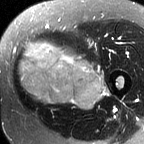
MRI of an extremity soft-tissue mass, one axial slice; slice 25 of 60 in the series (ordered by position); T2-weighted fat-saturated; MR volume resampled by the dataset authors to the PET/CT grid (not the native acquisition matrix); 144 × 144 image matrix, field of view 141 × 141 mm. Female patient. Case-level facts recorded for this patient, not image findings: histological type: pleiomorphic leiomyosarcoma; grade: intermediate; site of the primary tumour: left thigh.
Structures marked on this image (expert contour drawn on MRI and transferred to this co-registered scan by the dataset authors):
- gross tumour volume including surrounding oedema: bounding box (x1, y1, x2, y2) in pixels: (16, 40, 108, 111)
- gross tumour volume (mass): (18, 42, 103, 109)